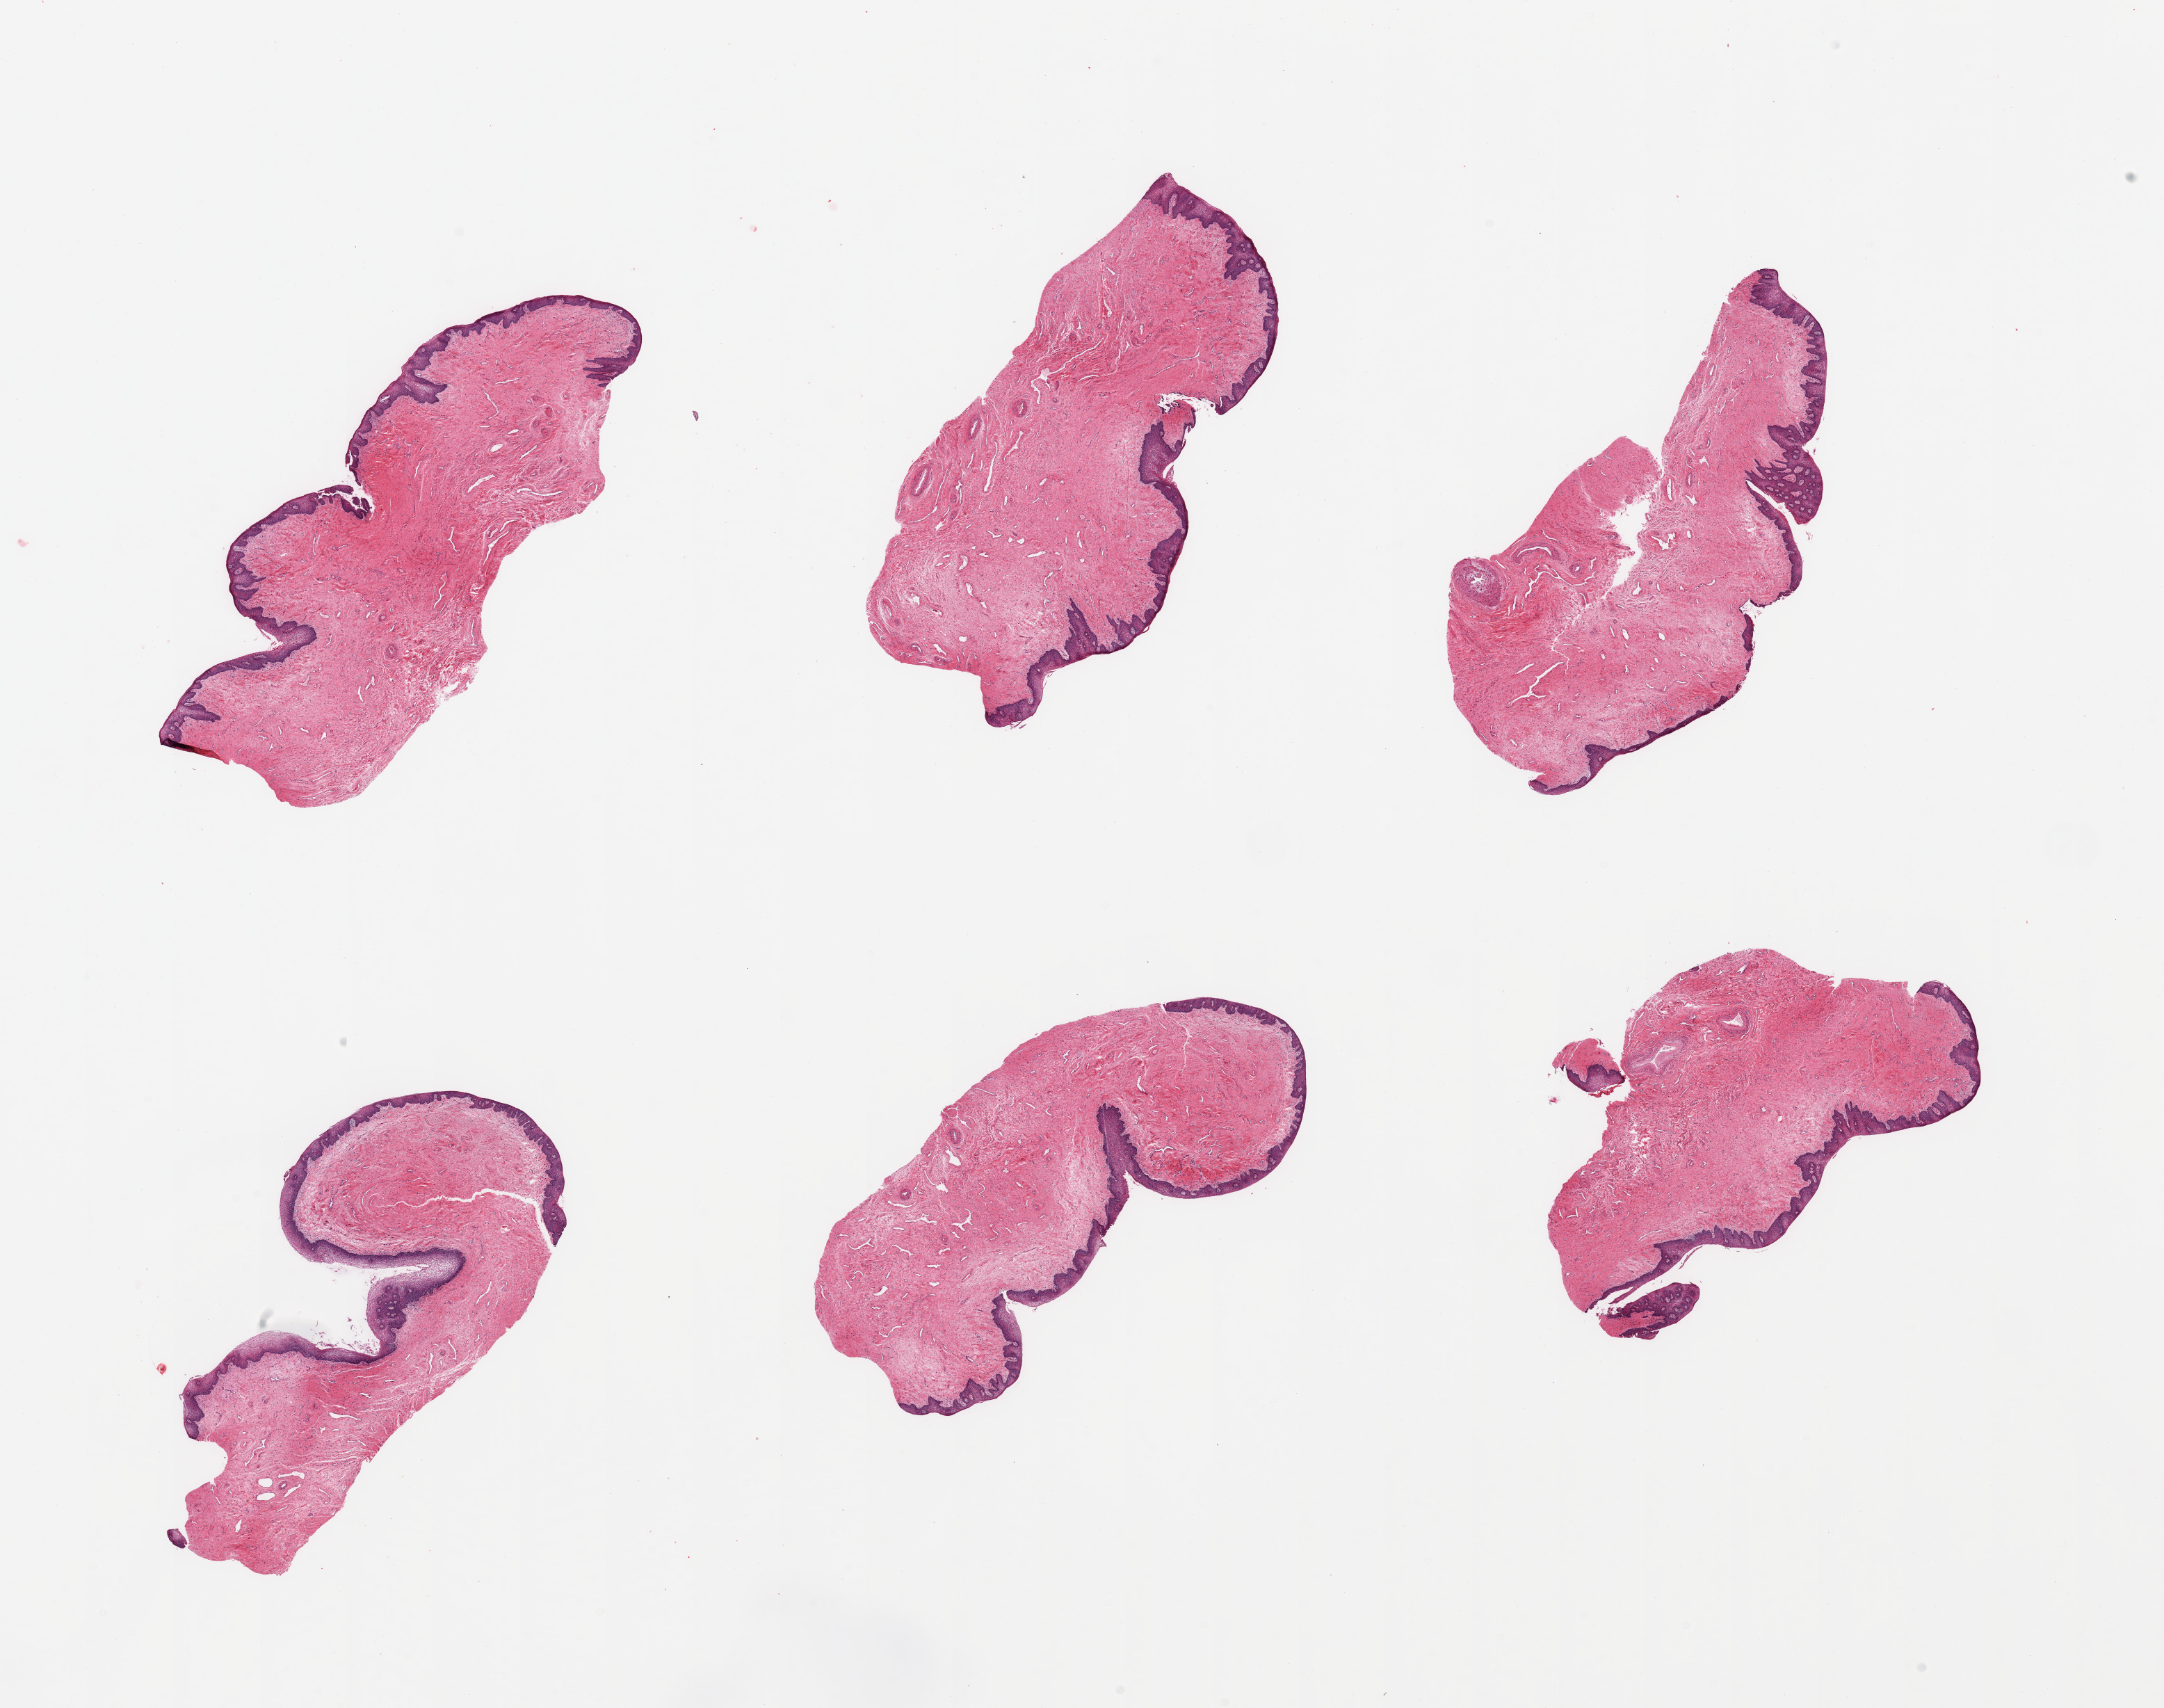
Hematoxylin and eosin (H&E) whole-slide image, brightfield — low-resolution overview of the scanned area, about 24.6 x 19.4 mm (acquisition: 20x scan); PAXgene-fixed, paraffin-embedded tissue; target tissue: vagina; tissue donor sample. Donor sex: female.
• reviewer comment on this tissue sample: 6 pieces, squamous mucosa up to ~0.25mm